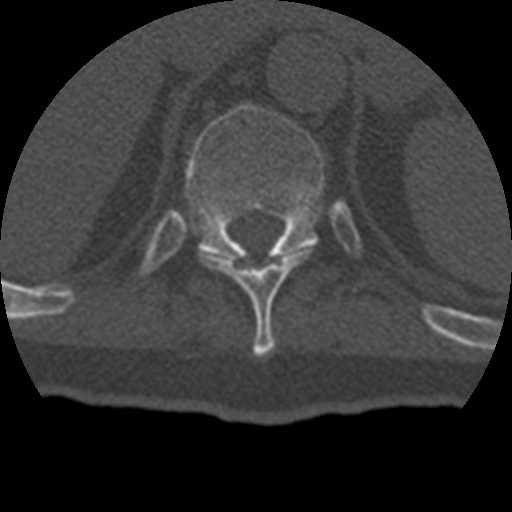
CT including the spine, one axial slice; position 207 of 399 along the scan axis; 120 kVp; bone window (W 1800 / L 400 HU); 512 × 512 image matrix, field of view 160 × 160 mm. Patient age 69 years. From the clinical record (not read from this slice): primary cancer: prostate.
Annotated regions visible in this slice (semi-automatic segmentation, software-assisted and operator-edited):
- T10 vertebra: box from (x=202, y=249) to (x=308, y=356) px
- T11 vertebra: (x=186, y=104)–(x=325, y=260)